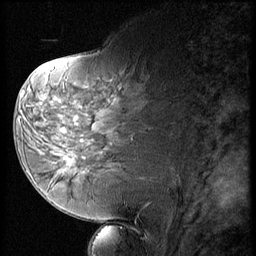
Breast MRI (dynamic contrast-enhanced), one sagittal slice; position 27 of 56 along the scan axis; 3 images stored at this slice position (order not interpretable as contrast timing); 1.5 T; TE 4.2 ms, TR 9 ms; 2.5 mm slice thickness; 256 × 256 image matrix, field of view 180 × 180 mm. Female patient, age 58 years. Case-level facts recorded for this patient, not image findings: setting: breast cancer imaged before/during neoadjuvant chemotherapy; receptor status: HR-positive, HER2-negative.
Annotated regions visible in this slice (semi-automatically segmented with operator editing):
- analysis volume of interest (the breast-tissue region the enhancement analysis was run in; not a lesion): bounding box [x1, y1, x2, y2] px = [47, 136, 88, 178]
- tumour enhancement mask (voxels above the 140 % enhancement threshold inside the analysis volume of interest): [65, 158, 75, 166]